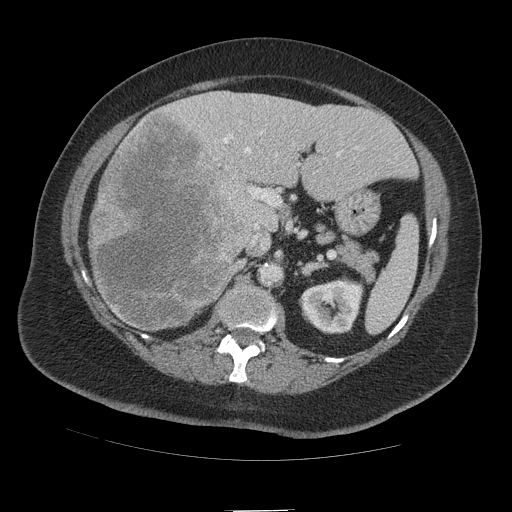
Contrast-enhanced abdominal CT (liver protocol), one axial slice; position 57 of 109 along the scan axis; reconstruction kernel STANDARD; soft-tissue window (W 400 / L 40 HU); 2.5 mm slice thickness; 512 × 512 image matrix, field of view 420 × 420 mm. Case-level facts recorded for this patient, not image findings: diagnosis: hepatocellular carcinoma (patient treated with transarterial chemoembolisation; whether this scan precedes or follows treatment is not stated here); TNM stage (as recorded): Stage-IVB; Child-Pugh class: A; tumour differentiation: poorly differentiated; tumour nodularity: multinodular.
Outlined on this slice (semi-automatically segmented with operator editing):
- liver parenchyma outside the tumour (the mass and vessels are separate outlines, so this box may not span the whole liver): bounding box (x1, y1, x2, y2) in pixels: (90, 90, 414, 328)
- mass: (88, 109, 253, 331)
- liver vessels: (223, 131, 342, 243)